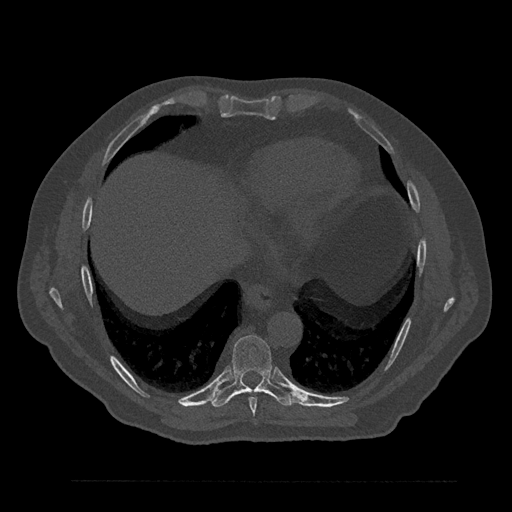
CT including the spine, one axial slice. Slice 420 of 797 in the series (ordered by position). Reconstruction kernel Br40s/3. 120 kVp. Bone window (W 1800 / L 400 HU). 0.5 mm slice thickness. 512 × 512 image matrix, field of view 430 × 430 mm. Patient: male, 61 years. Case-level facts recorded for this patient, not image findings: primary cancer: prostate.
Annotated regions visible in this slice (semi-automatic segmentation, software-assisted and operator-edited):
- T8 vertebra: bounding box [x1, y1, x2, y2] px = [249, 397, 257, 416]
- T9 vertebra: [212, 335, 295, 407]